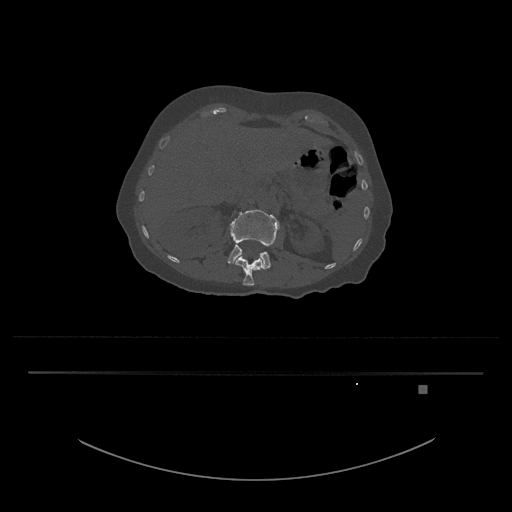
CT including the spine, one axial slice. Position 521 of 797 along the scan axis. Reconstruction kernel Br40s/3. Bone window (W 1800 / L 400 HU). 512 × 512 image matrix, field of view 500 × 500 mm. Patient: female, 57 years. Case-level facts recorded for this patient, not image findings: primary cancer: cervical.
Annotated regions visible in this slice (semi-automatically segmented with operator editing):
- L1 vertebra: bounding box (x1, y1, x2, y2) in pixels: (235, 255, 263, 286)